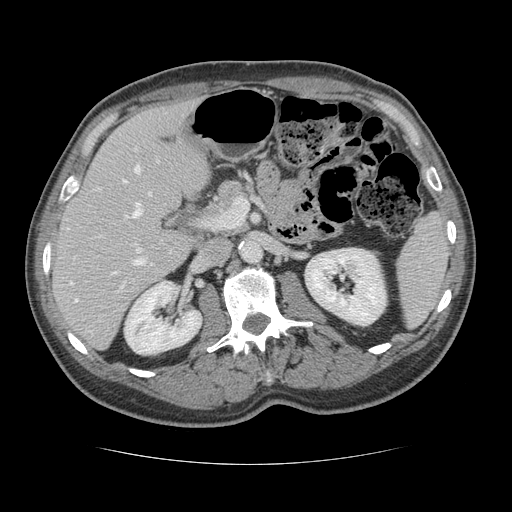
Contrast-enhanced abdominal CT, one axial slice. Position 69 of 134 along the scan axis. 120 kVp. Intravenous contrast given. Soft-tissue window (W 400 / L 40 HU). 2.5 mm slice thickness. 512 × 512 image matrix, field of view 377 × 377 mm. Male patient, age 68 years. From the clinical record (not read from this slice): diagnosis: colorectal cancer liver metastases, imaged before liver resection; multiple liver metastases: yes; largest metastasis: 2.2 cm; chemotherapy before resection: no.
Outlined on this slice (expert manual segmentation):
- hepatic veins: bounding box [x1, y1, x2, y2] px = [70, 166, 152, 301]
- liver: [53, 101, 211, 348]
- planned liver remnant (the part of the liver to remain after resection): [53, 101, 211, 337]
- portal vein (with intrahepatic branches): [113, 216, 152, 286]